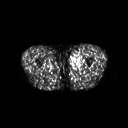
FDG PET of an extremity soft-tissue mass (from a PET/CT study), one axial slice. Position 247 of 311 along the scan axis. 3.27 mm slice thickness. 128 × 128 image matrix, field of view 500 × 500 mm. Patient: male, 29 years. Case-level facts recorded for this patient, not image findings: histological type: mixoid liposarcoma; grade: low; site of the primary tumour: left thigh.
Structures marked on this image (expert contour drawn on MRI and transferred to this co-registered scan by the dataset authors):
- gross tumour volume (mass): bounding box <70,53,83,68> (left, top, right, bottom; pixels)